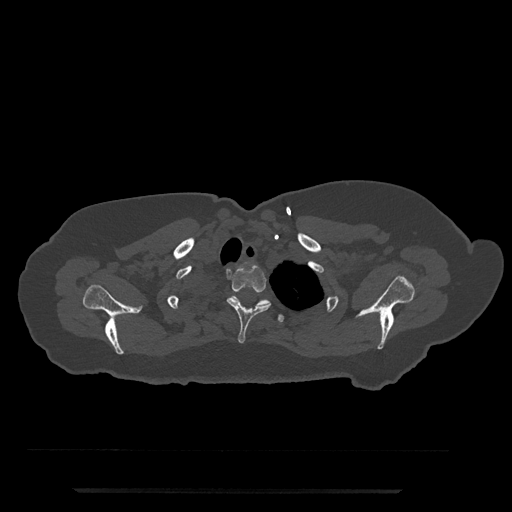
CT including the spine, one axial slice; slice 666 of 797 in the series (ordered by position); reconstruction kernel Br40s/3; bone window (W 1800 / L 400 HU); 0.5 mm slice thickness; 512 × 512 image matrix. Patient: female, 51 years. From the clinical record (not read from this slice): primary cancer: neuro; vertebrae with lytic lesions (as recorded): T8.
Outlined on this slice (semi-automatically segmented with operator editing):
- T2 vertebra: bounding box (x1, y1, x2, y2) in pixels: (227, 265, 271, 343)
- T3 vertebra: (232, 295, 284, 323)